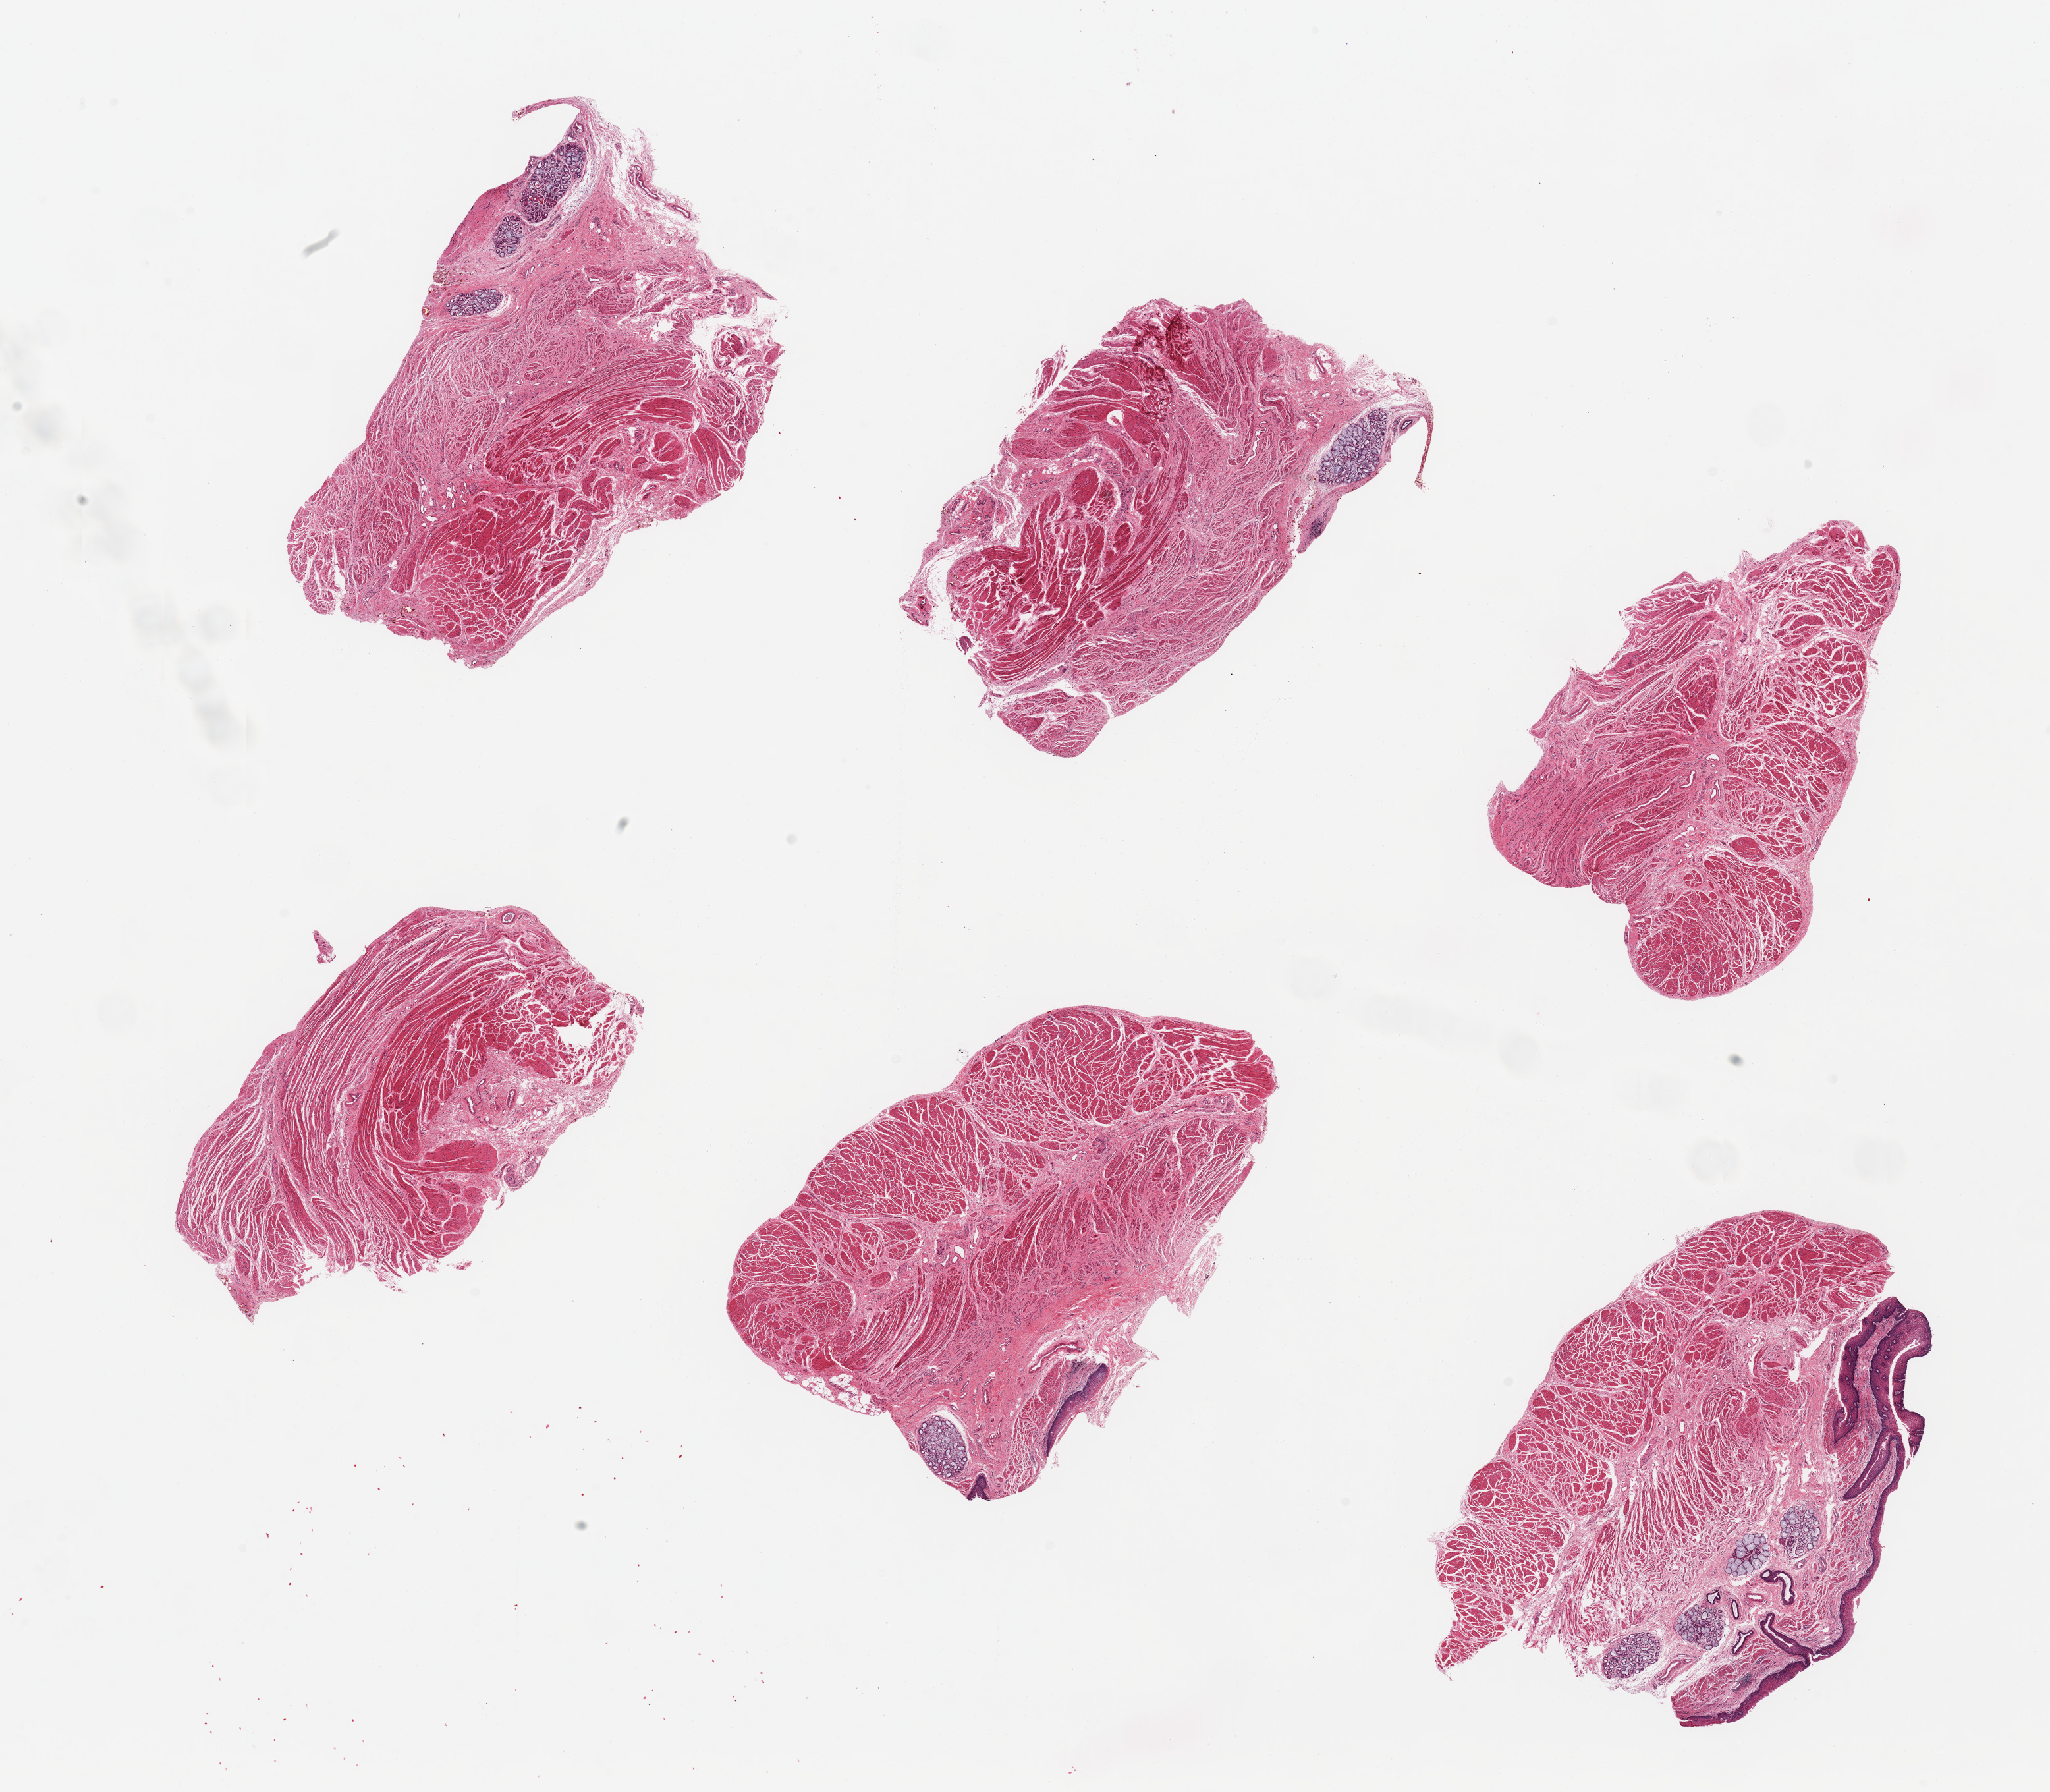
Digitized haematoxylin and eosin-stained section, whole scanned area (about 24.6 x 21.5 mm, from a 20x scan) shown as a low-resolution overview. PAXgene-fixed paraffin-embedded (PFPE) section. Target tissue: gastroesophageal junction. Donor tissue sample.
Reviewer comment on this tissue sample: 6 pieces, trace residual squamous mucosa and mucous glands.